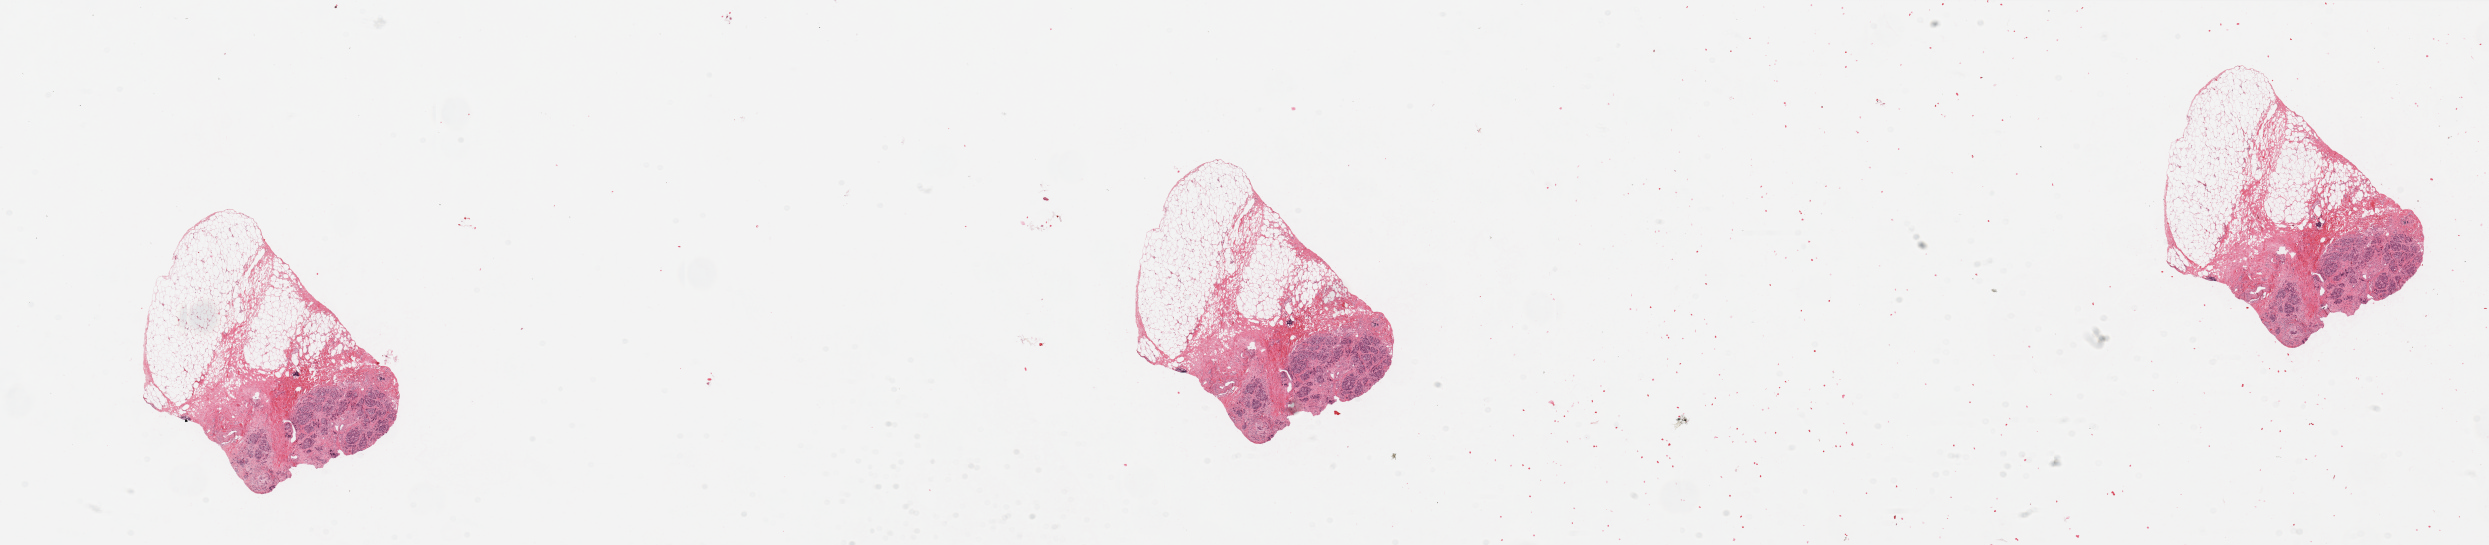
Digitized Hematoxylin and eosin (H&E) stained tissue section (whole slide), low-resolution overview of the scanned area, about 39.4 x 8.6 mm. Normal (non-tumour) tissue sample, sampled site: pancreas. Patient: male, age 55 years.
This section: normal (non-tumour) tissue from the same patient. Patient diagnosis: Infiltrating duct carcinoma, NOS.